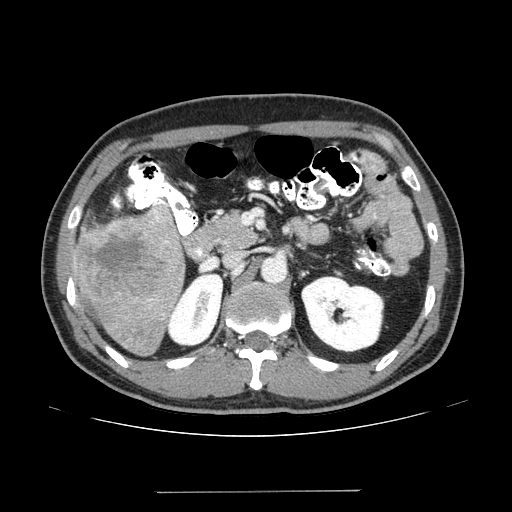
Contrast-enhanced abdominal CT (liver protocol), one axial slice; slice 67 of 131 in the series (ordered by position); reconstruction kernel STANDARD; one of 2 acquisitions stored at this slice position; soft-tissue window (W 400 / L 40 HU); 512 × 512 image matrix, field of view 380 × 380 mm. Case-level facts recorded for this patient, not image findings: diagnosis: hepatocellular carcinoma (patient treated with transarterial chemoembolisation; whether this scan precedes or follows treatment is not stated here); TNM stage (as recorded): Stage-I; Child-Pugh class: A; tumour differentiation: poorly differentiated; tumour size: 10.3 cm.
Structures marked on this image (semi-automatic segmentation, software-assisted and operator-edited):
- liver parenchyma outside the tumour (the mass and vessels are separate outlines, so this box may not span the whole liver): bounding box [x1, y1, x2, y2] px = [70, 206, 184, 356]
- mass: [74, 218, 183, 325]